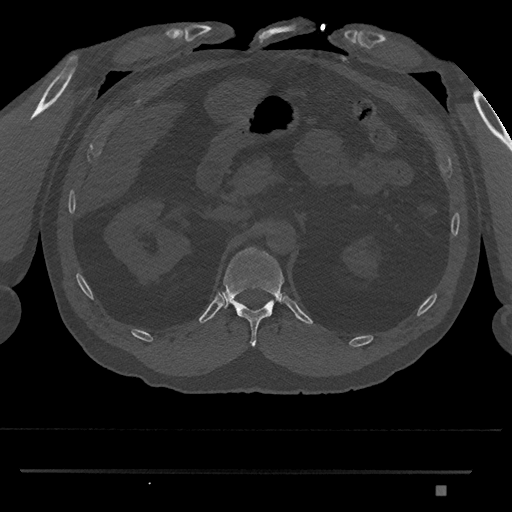
CT including the spine, one axial slice. Position 880 of 1134 along the scan axis. Reconstruction kernel Br40s/3. Bone window (W 1800 / L 400 HU). 0.5 mm slice thickness. 512 × 512 image matrix, field of view 429 × 429 mm. Patient: male, 65 years. Case-level facts recorded for this patient, not image findings: primary cancer: prostate.
Outlined on this slice (semi-automatically segmented with operator editing):
- T12 vertebra: bounding box <219,247,284,347> (left, top, right, bottom; pixels)